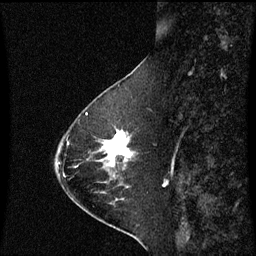
Breast MRI (dynamic contrast-enhanced), one sagittal slice; slice 21 of 60 in the series (ordered by position); dynamic contrast-enhanced series, image 2 of 3 at this slice position (ordered by acquisition); 1.5 T; TE 4.2 ms, TR 8.9 ms; 256 × 256 image matrix. Female patient, age 63 years. From the clinical record (not read from this slice): setting: breast cancer imaged before/during neoadjuvant chemotherapy; receptor status: HR-positive, HER2-negative.
Annotated regions visible in this slice (semi-automatically segmented with operator editing):
- analysis volume of interest (the breast-tissue region the enhancement analysis was run in; not a lesion): box from (x=94, y=130) to (x=134, y=177) px
- tumour enhancement mask (voxels above the 70 % enhancement threshold inside the analysis volume of interest): (x=103, y=132)–(x=132, y=167)